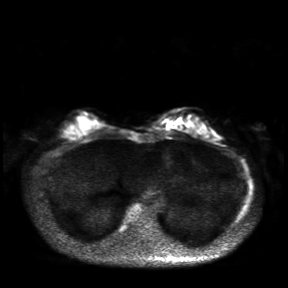
Breast MRI, one axial slice; slice 8 of 30 in the series (ordered by position); diffusion-weighted series; image 2 of 4 stored at this slice position (different b-values; order by instance number); 3 T; 4 mm slice thickness; 288 × 288 image matrix. Female patient.
Outlined on this slice (expert manual segmentation):
- tumour on diffusion-weighted imaging: box from (x=168, y=121) to (x=173, y=124) px